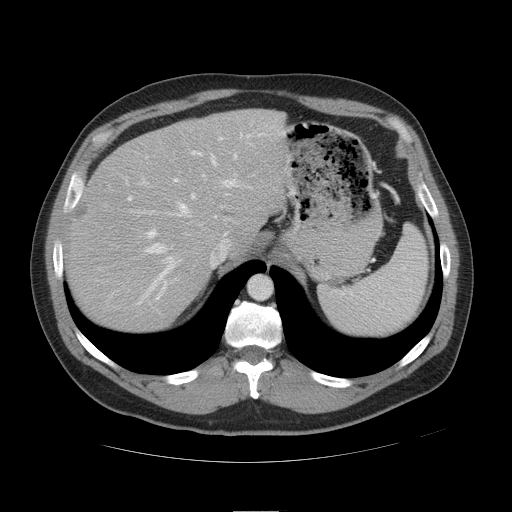
Contrast-enhanced abdominal CT, one axial slice; slice 35 of 49 in the series (ordered by position); reconstruction kernel STANDARD; 120 kVp; intravenous contrast given; soft-tissue window (W 400 / L 40 HU); 512 × 512 image matrix, field of view 425 × 425 mm. Male patient, age 52 years. From the clinical record (not read from this slice): diagnosis: colorectal cancer liver metastases, imaged before liver resection; multiple liver metastases: yes; largest metastasis: 5.1 cm.
Structures marked on this image (manually delineated by an expert):
- hepatic veins: bounding box <137,153,238,305> (left, top, right, bottom; pixels)
- liver: <69,111,284,331>
- planned liver remnant (the part of the liver to remain after resection): <135,111,284,245>
- portal vein (with intrahepatic branches): <126,133,266,239>
- liver metastasis: <76,202,90,218>